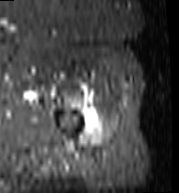
MRI of an extremity soft-tissue mass, one axial slice. Slice 97 of 103 in the series (ordered by position). STIR. MR volume resampled by the dataset authors to the PET/CT grid (not the native acquisition matrix). 3.27 mm slice thickness. 179 × 193 image matrix, field of view 175 × 188 mm. Female patient. Case-level facts recorded for this patient, not image findings: histological type: undifferentiated – high grade; grade: high; site of the primary tumour: left thigh.
Annotated regions visible in this slice (expert contour drawn on MRI and transferred to this co-registered scan by the dataset authors):
- gross tumour volume including surrounding oedema: bounding box <88,121,101,134> (left, top, right, bottom; pixels)